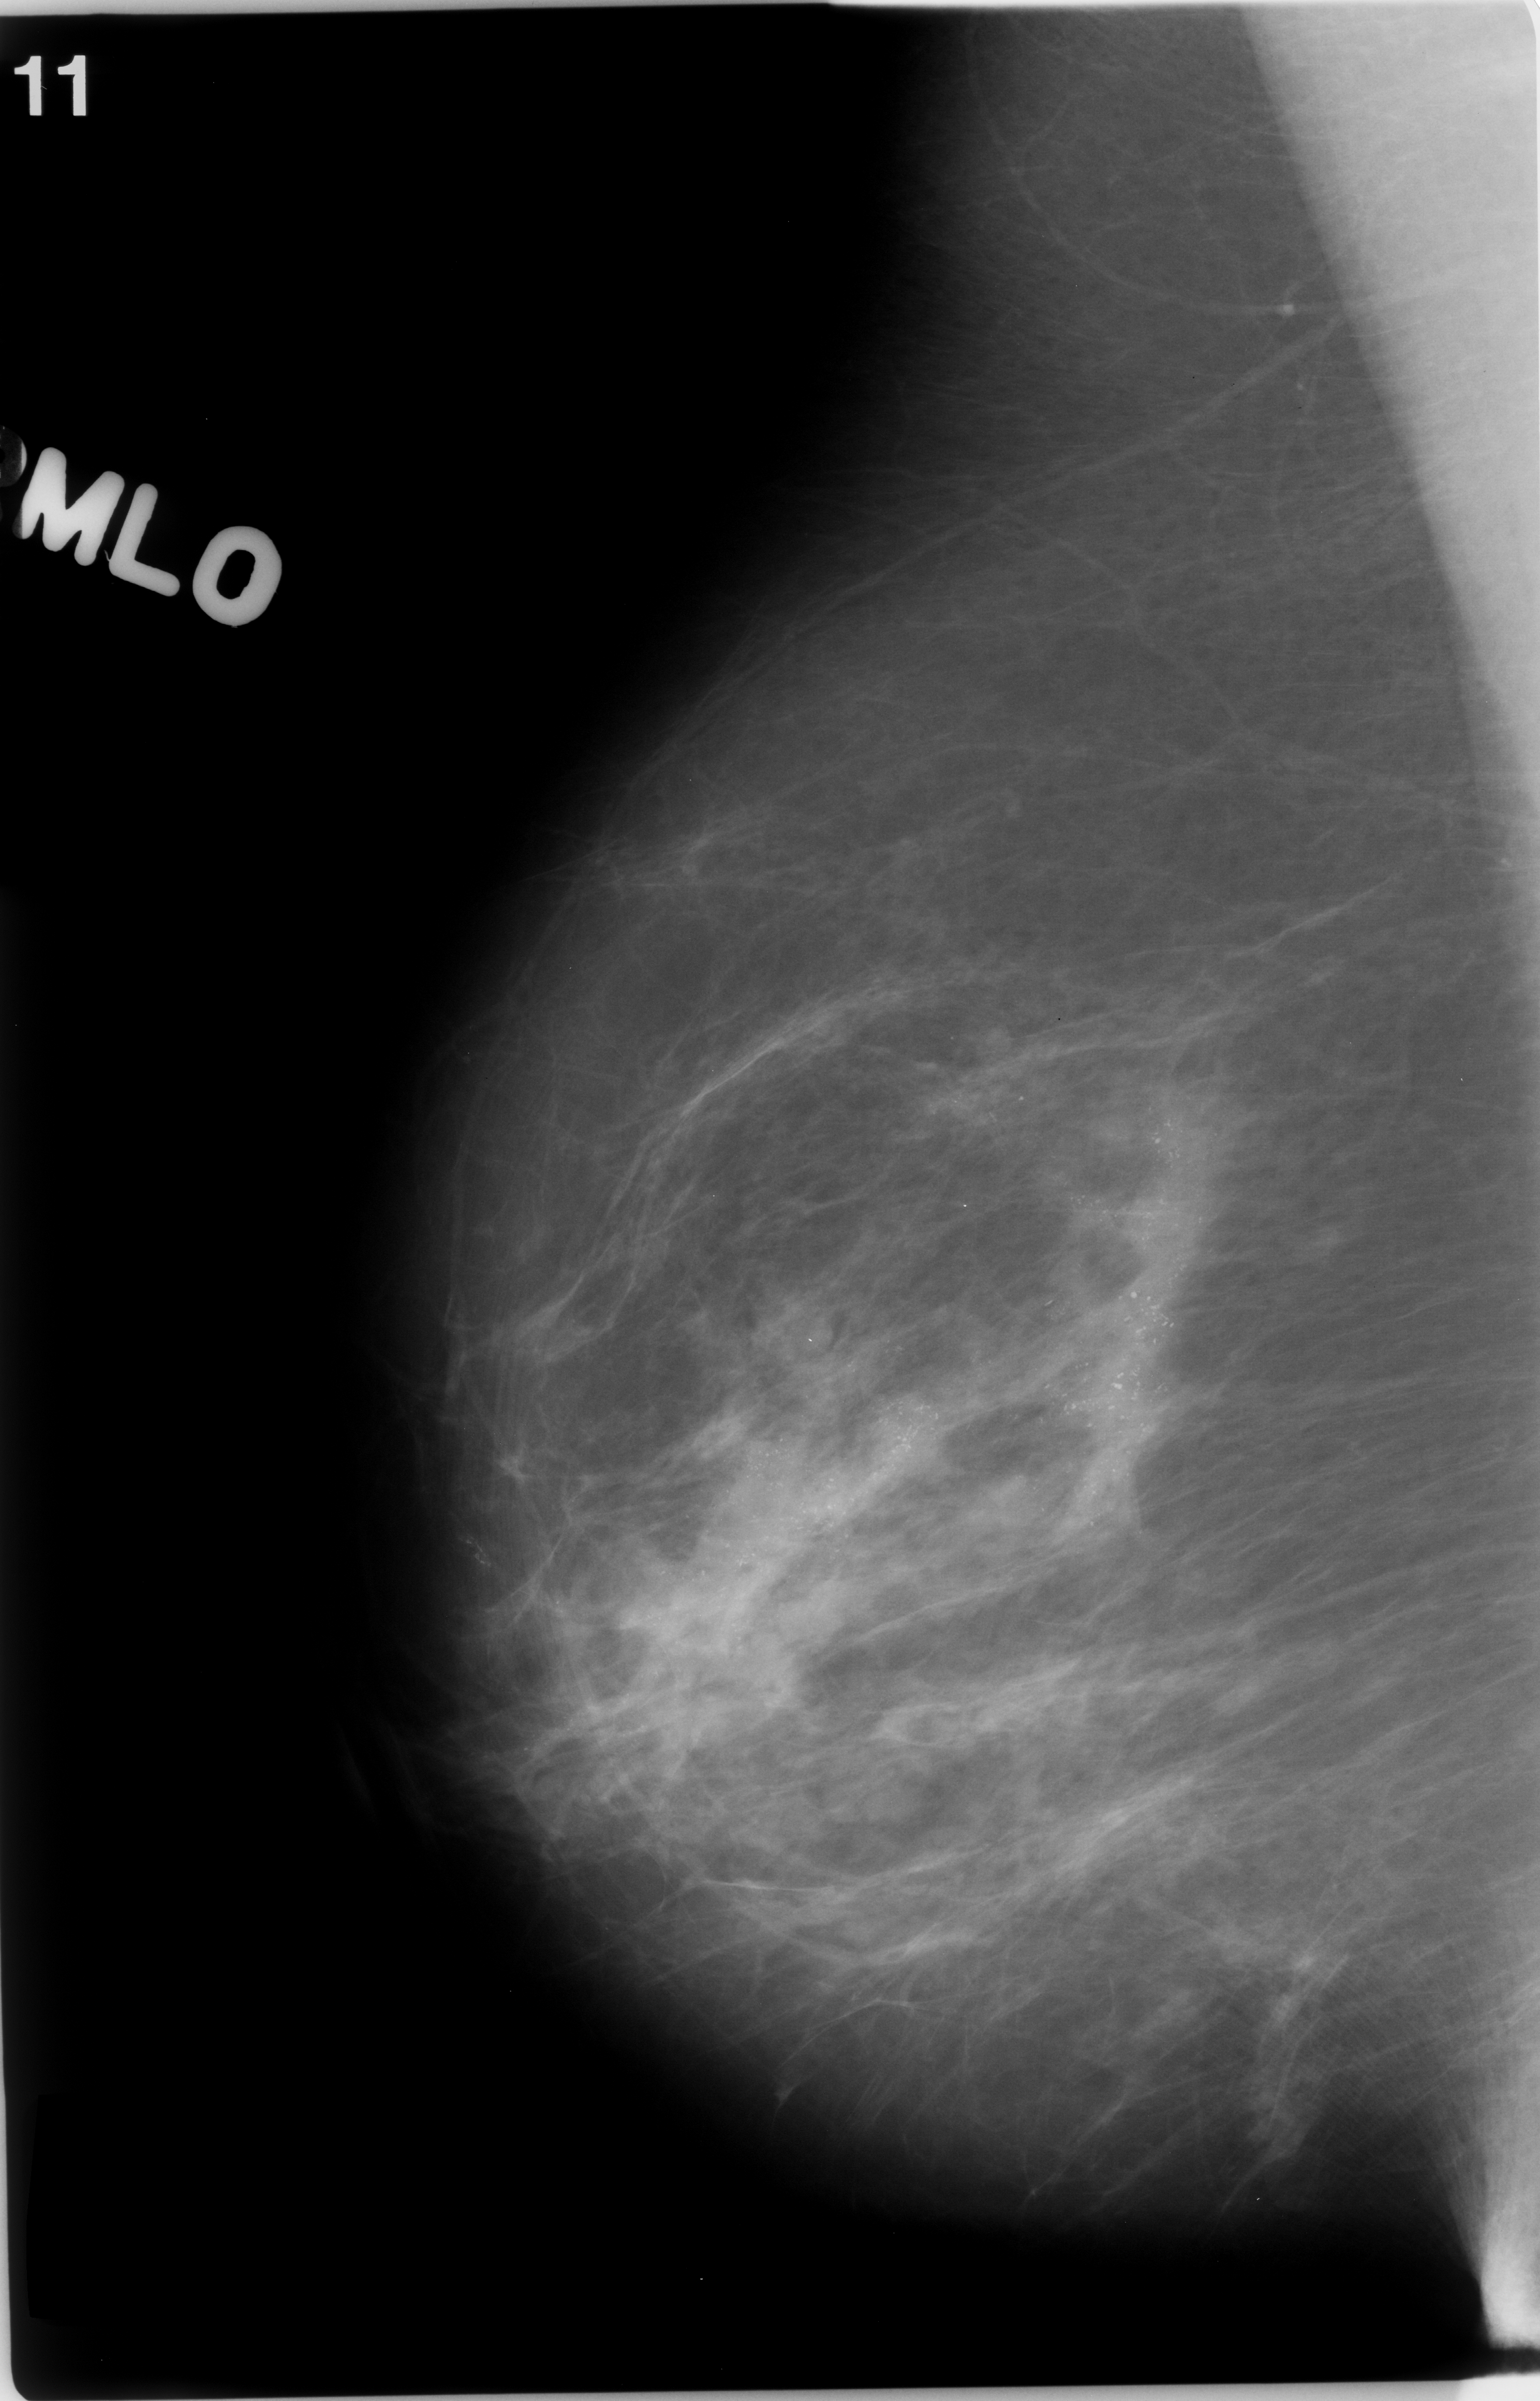
Scanned film-screen mammogram, right breast, MLO view.
Abnormality record for this image: calcifications, morphology pleomorphic, distribution regional; BI-RADS assessment category 5; subtlety rating 5 on a 1 (subtle) to 5 (obvious) scale; pathology result (as recorded, not read from the image): malignant.